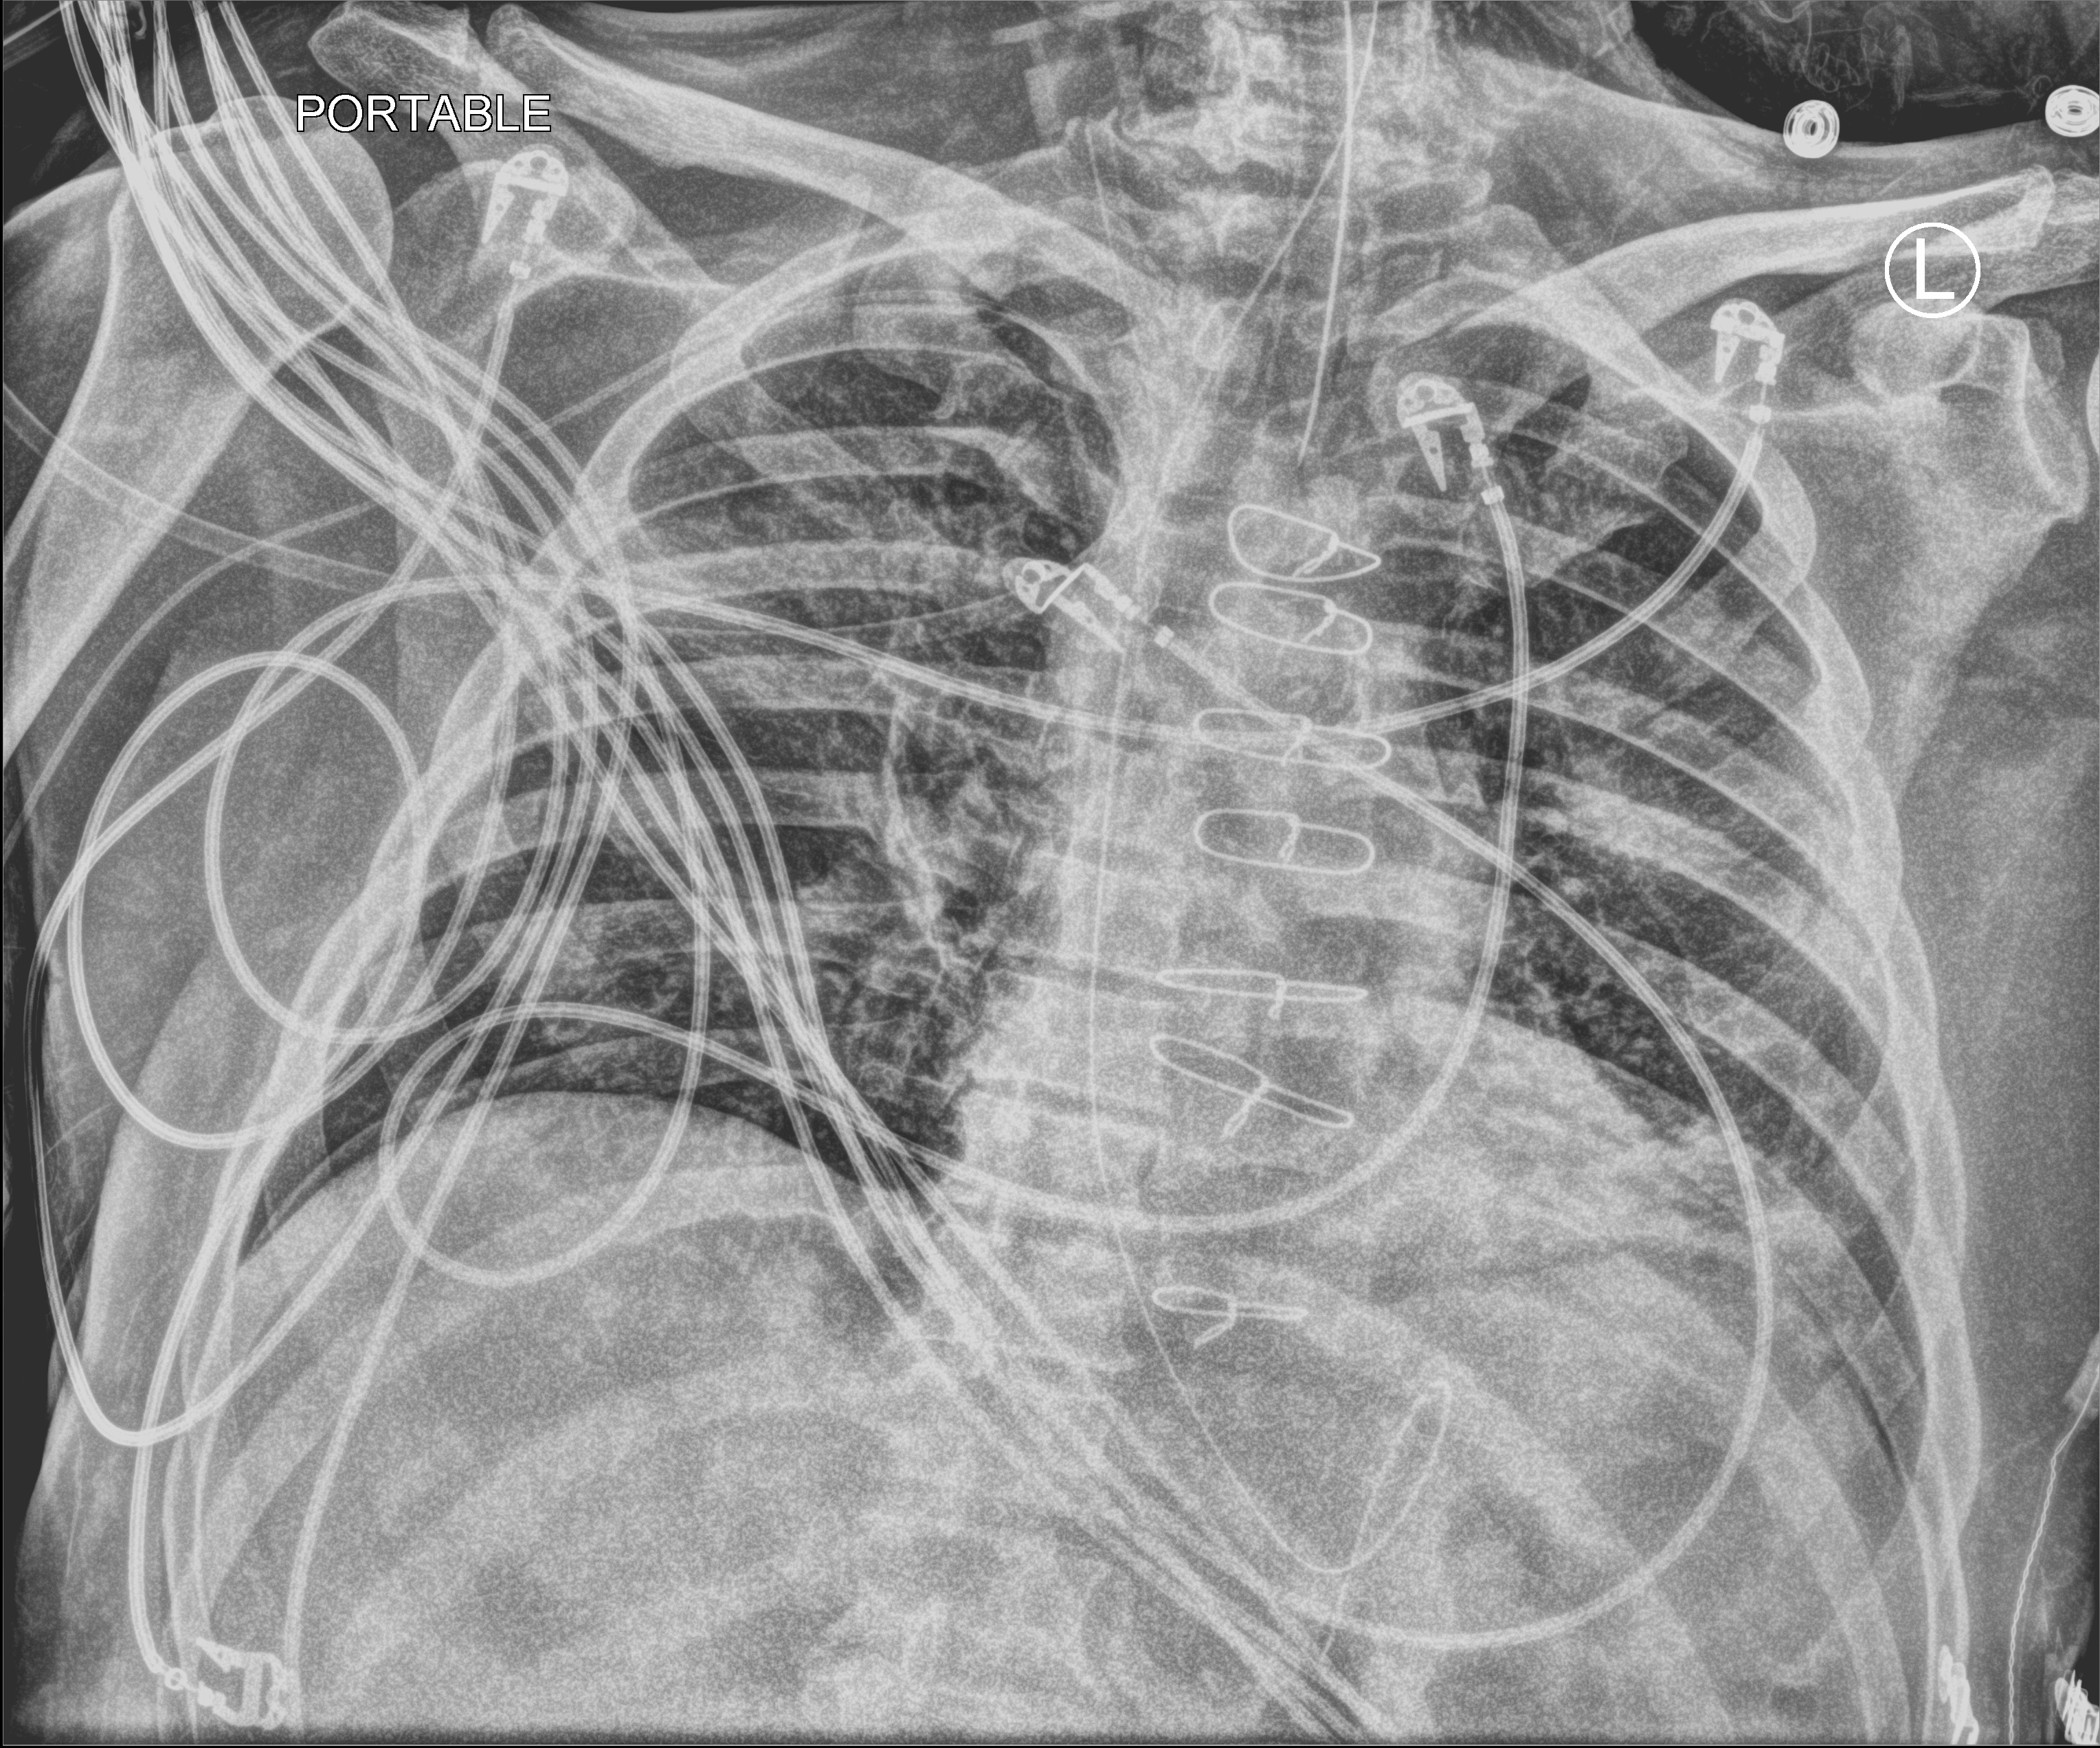
Bedside chest radiograph (computed radiography), anteroposterior (AP) projection. Male patient hospitalised with COVID-19, age 60–74 years.
Hospital-stay facts (about this admission, not read from this image; timing relative to this image not recorded): mechanically ventilated during this hospital stay: yes; smoking status (admission record): former.